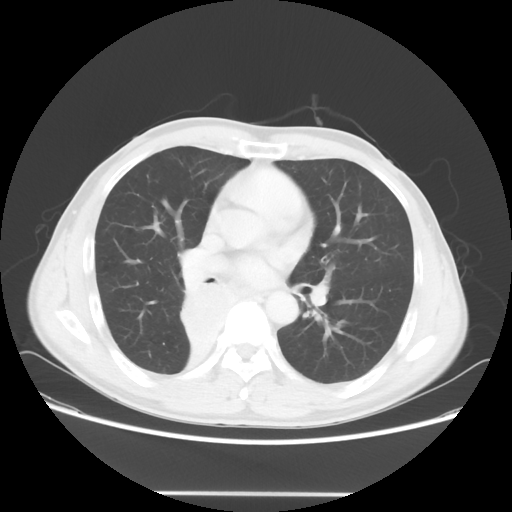
Chest CT, one axial slice. Reconstruction kernel STANDARD. Lung window (W 1500 / L -600 HU). 5 mm slice thickness. 512 × 512 image matrix, field of view 393 × 393 mm. Male patient, age 47 years. From the clinical record (not read from this slice): clinical TNM (as recorded): T2 N0 M0.
Structures marked on this image (rectangle marked by the reading radiologist):
- lung tumour (recorded histology: squamous cell carcinoma): bounding box [x1, y1, x2, y2] px = [175, 281, 239, 348]